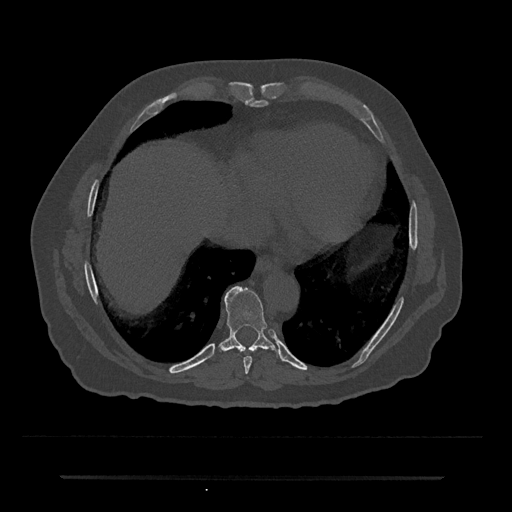
CT including the spine, one axial slice; slice 291 of 797 in the series (ordered by position); bone window (W 1800 / L 400 HU); 0.5 mm slice thickness; 512 × 512 image matrix, field of view 437 × 437 mm. Male patient, age 69 years. From the clinical record (not read from this slice): primary cancer: prostate.
Outlined on this slice (semi-automatically segmented with operator editing):
- T8 vertebra: bounding box <243,356,252,373> (left, top, right, bottom; pixels)
- T9 vertebra: <218,286,278,354>